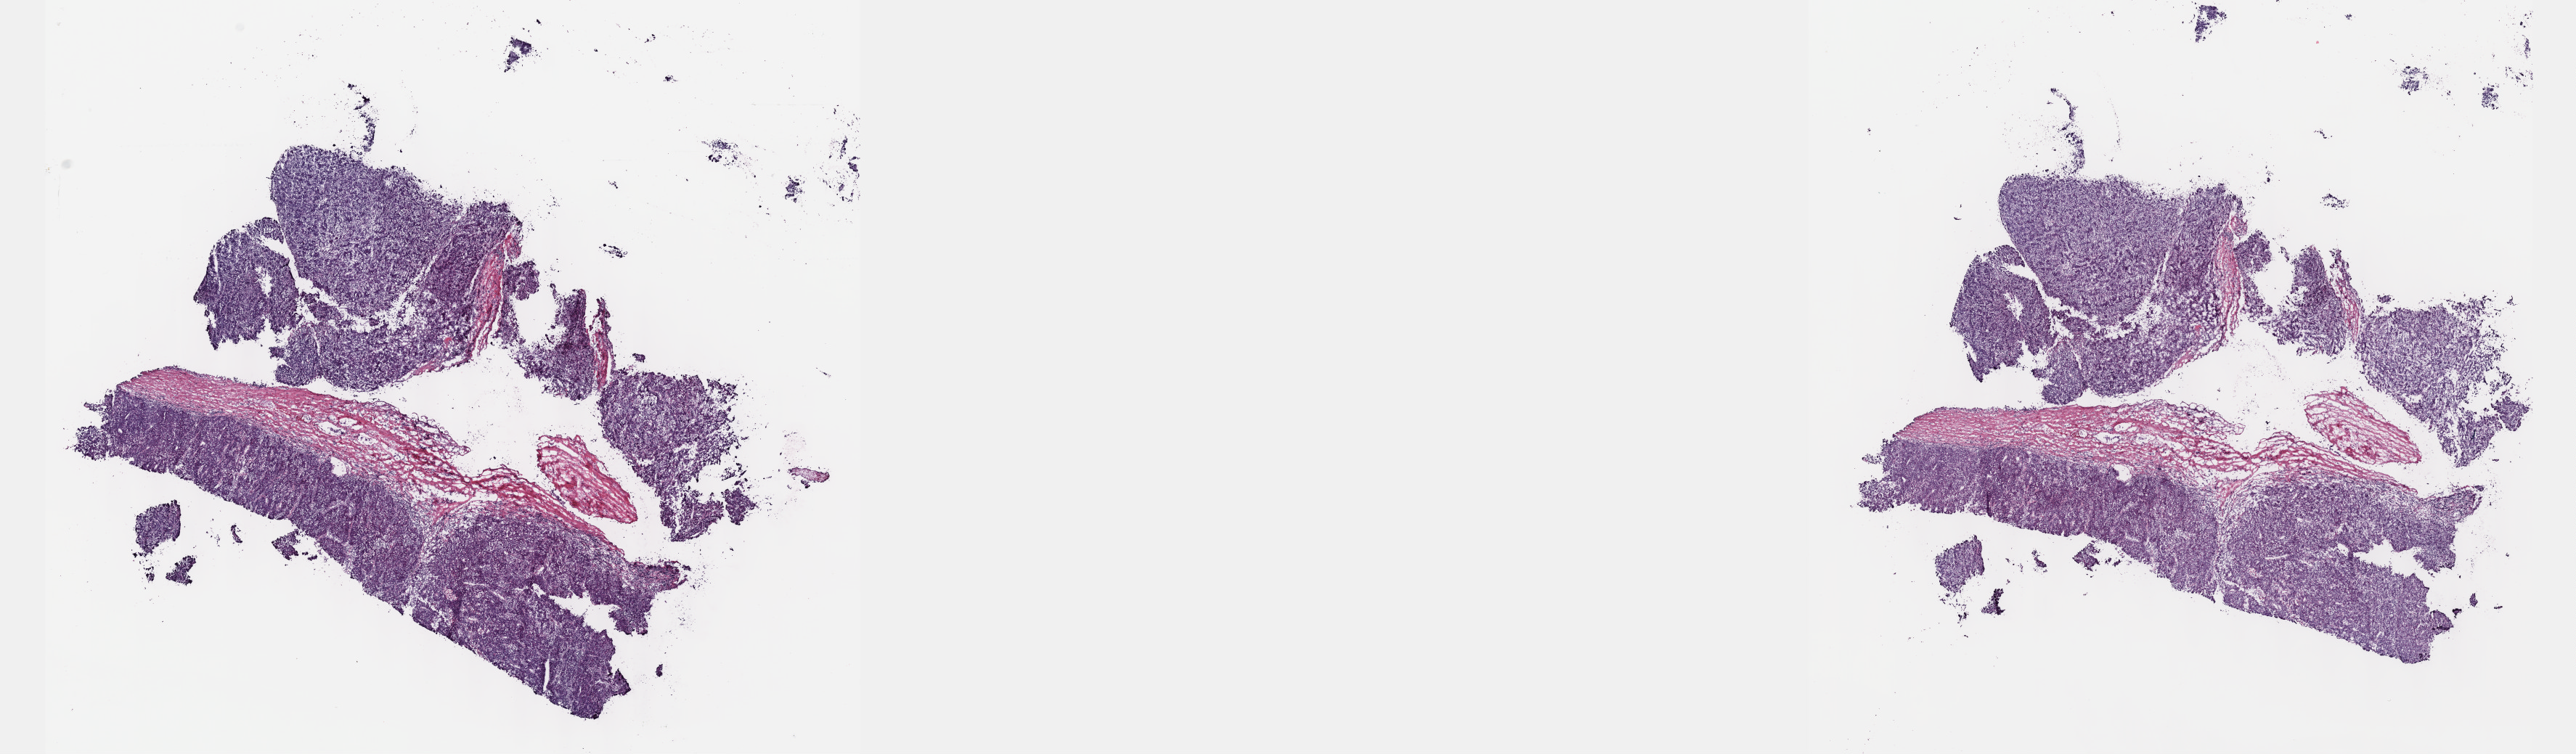
Whole-slide histology image, Hematoxylin and eosin (H&E) stained — shown as a low-resolution overview of the whole scanned area (about 28.7 x 8.4 mm, slide scanned at 40x), frozen section from the top of the tissue portion, primary tumour sample from the liver. Patient: male, age at initial diagnosis 69 years. Histologic grade: G2 (moderately differentiated). Slide review estimates, as recorded: tumour cells 65%, tumour nuclei 70%, normal cells 0%, stromal cells 30%, necrosis 5%. Inflammatory infiltration, as recorded: lymphocyte infiltration 20%, monocyte infiltration 2%, neutrophil infiltration 2%.
* pathologic diagnosis: Hepatocellular carcinoma, NOS
* AJCC pathologic stage: II (7th edition)